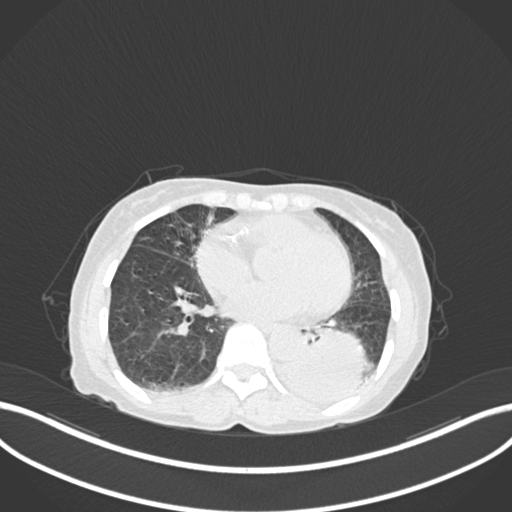
Chest CT, one axial slice; slice 49 of 233 in the series (ordered by position); reconstruction kernel B30f; lung window (W 1500 / L -600 HU); 1 mm slice thickness; 512 × 512 image matrix, field of view 400 × 400 mm. Female patient, age 78 years. From the clinical record (not read from this slice): clinical TNM (as recorded): T3 N0 M1.
Structures marked on this image (bounding box drawn by a radiologist):
- lung tumour (recorded histology: squamous cell carcinoma): bounding box (x1, y1, x2, y2) in pixels: (279, 319, 376, 403)